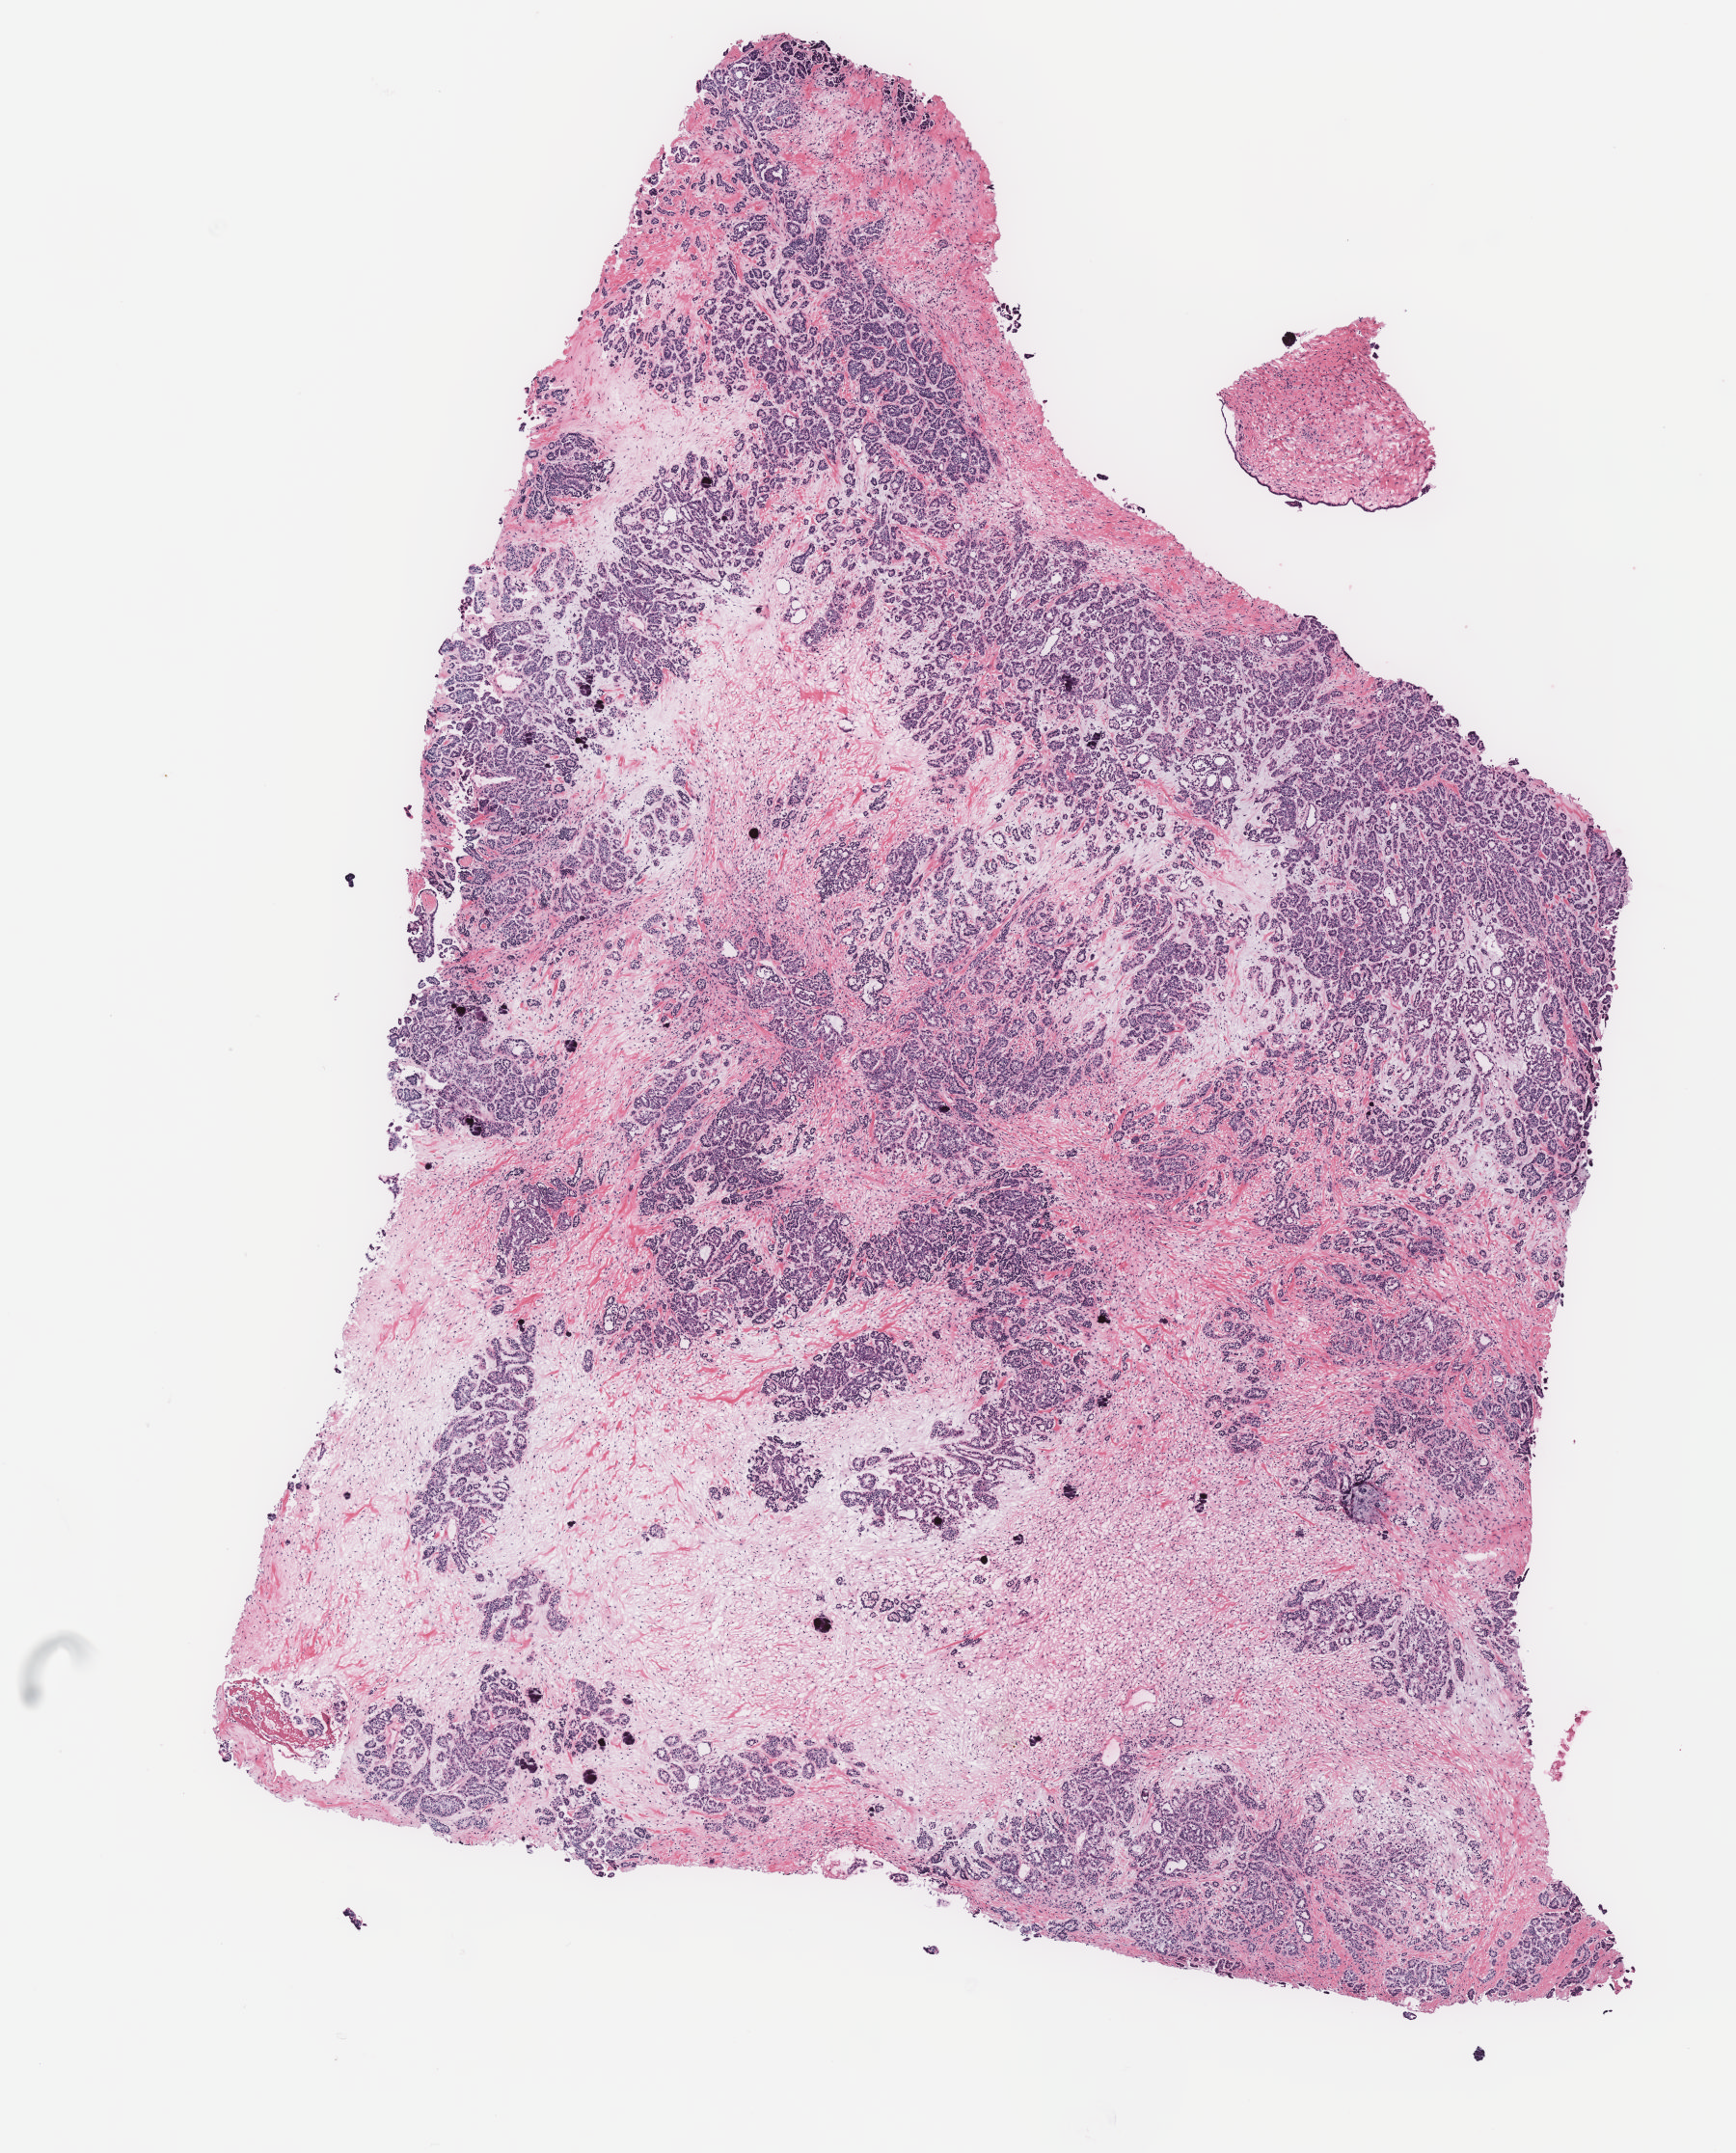
Whole-slide histology image, H&E — shown as a low-resolution overview of the whole scanned area (about 7.2 x 8.9 mm, acquisition: 40x scan). Ovary, tumour tissue. Female, 57 y/o.
Diagnosis: Serous adenocarcinoma, NOS. Primary tumour site (as recorded): ovary.